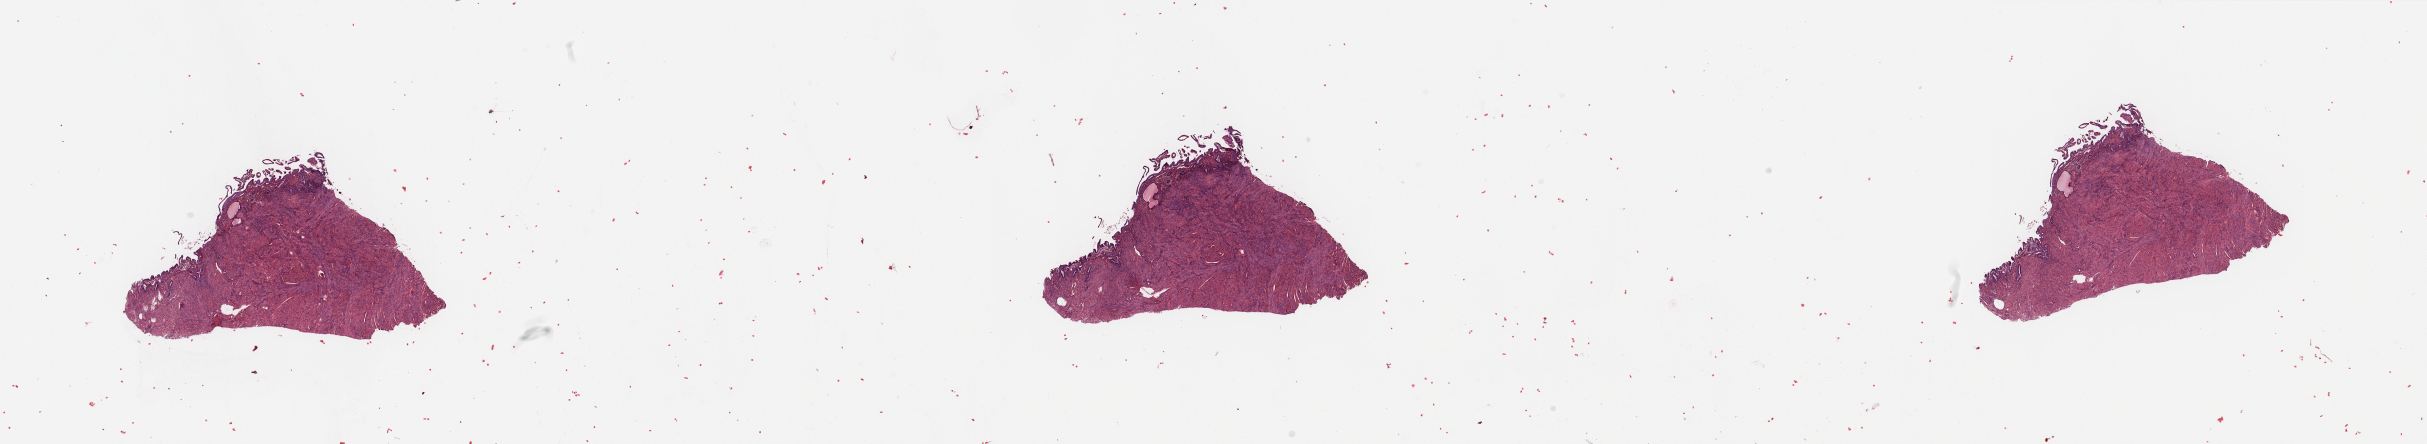
H&E-stained whole-slide image — a low-resolution overview of the entire scanned area, about 38.4 x 7.0 mm (acquisition: 20x scan); normal (non-tumour) tissue sample, sampled site: uterus. 69-year-old female patient.
This section: normal (non-tumour) tissue from the same patient. Patient diagnosis: Endometrioid adenocarcinoma, NOS.